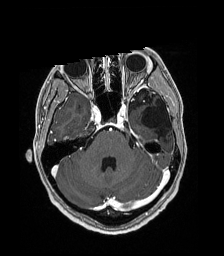
Brain MRI from a brain-tumour surgery series, one axial slice. Position 127 of 192 along the scan axis. T1-weighted post-contrast. 1 mm slice thickness. 224 × 256 image matrix. Case-level facts recorded for this patient, not image findings: histopathology: Low grade glioma; IDH mutation: no; tumour location: Left Parieto-Occipital Intraventricular.
Outlined on this slice (manually delineated by an expert):
- previous resection cavity: bounding box (x1, y1, x2, y2) in pixels: (141, 99, 171, 136)